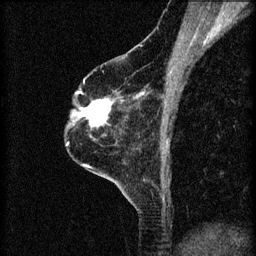
Breast MRI (dynamic contrast-enhanced), one sagittal slice. Slice 43 of 60 in the series (ordered by position). 3 images stored at this slice position (order not interpretable as contrast timing). 1.5 T. TE 4.2 ms, TR 8.2 ms. 256 × 256 image matrix. Patient: female, 60 years.
Outlined on this slice (semi-automatic segmentation, software-assisted and operator-edited):
- analysis volume of interest (the breast-tissue region the enhancement analysis was run in; not a lesion): bounding box <78,94,113,129> (left, top, right, bottom; pixels)
- tumour enhancement mask (voxels above the 70 % enhancement threshold inside the analysis volume of interest): <78,94,112,127>